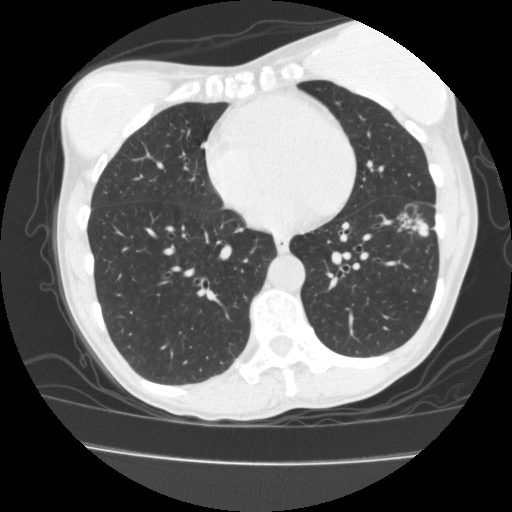
Low-dose screening chest CT, one axial slice; slice 65 of 171 in the series (ordered by position); reconstruction kernel FC10; 120 kVp; lung window (W 1500 / L -600 HU); 2 mm slice thickness; 512 × 512 image matrix, field of view 339 × 339 mm.
Outlined on this slice (outlined manually by an expert reader):
- lesion 1 (tumor, lower lobe of left lung): box from (x=412, y=219) to (x=428, y=235) px